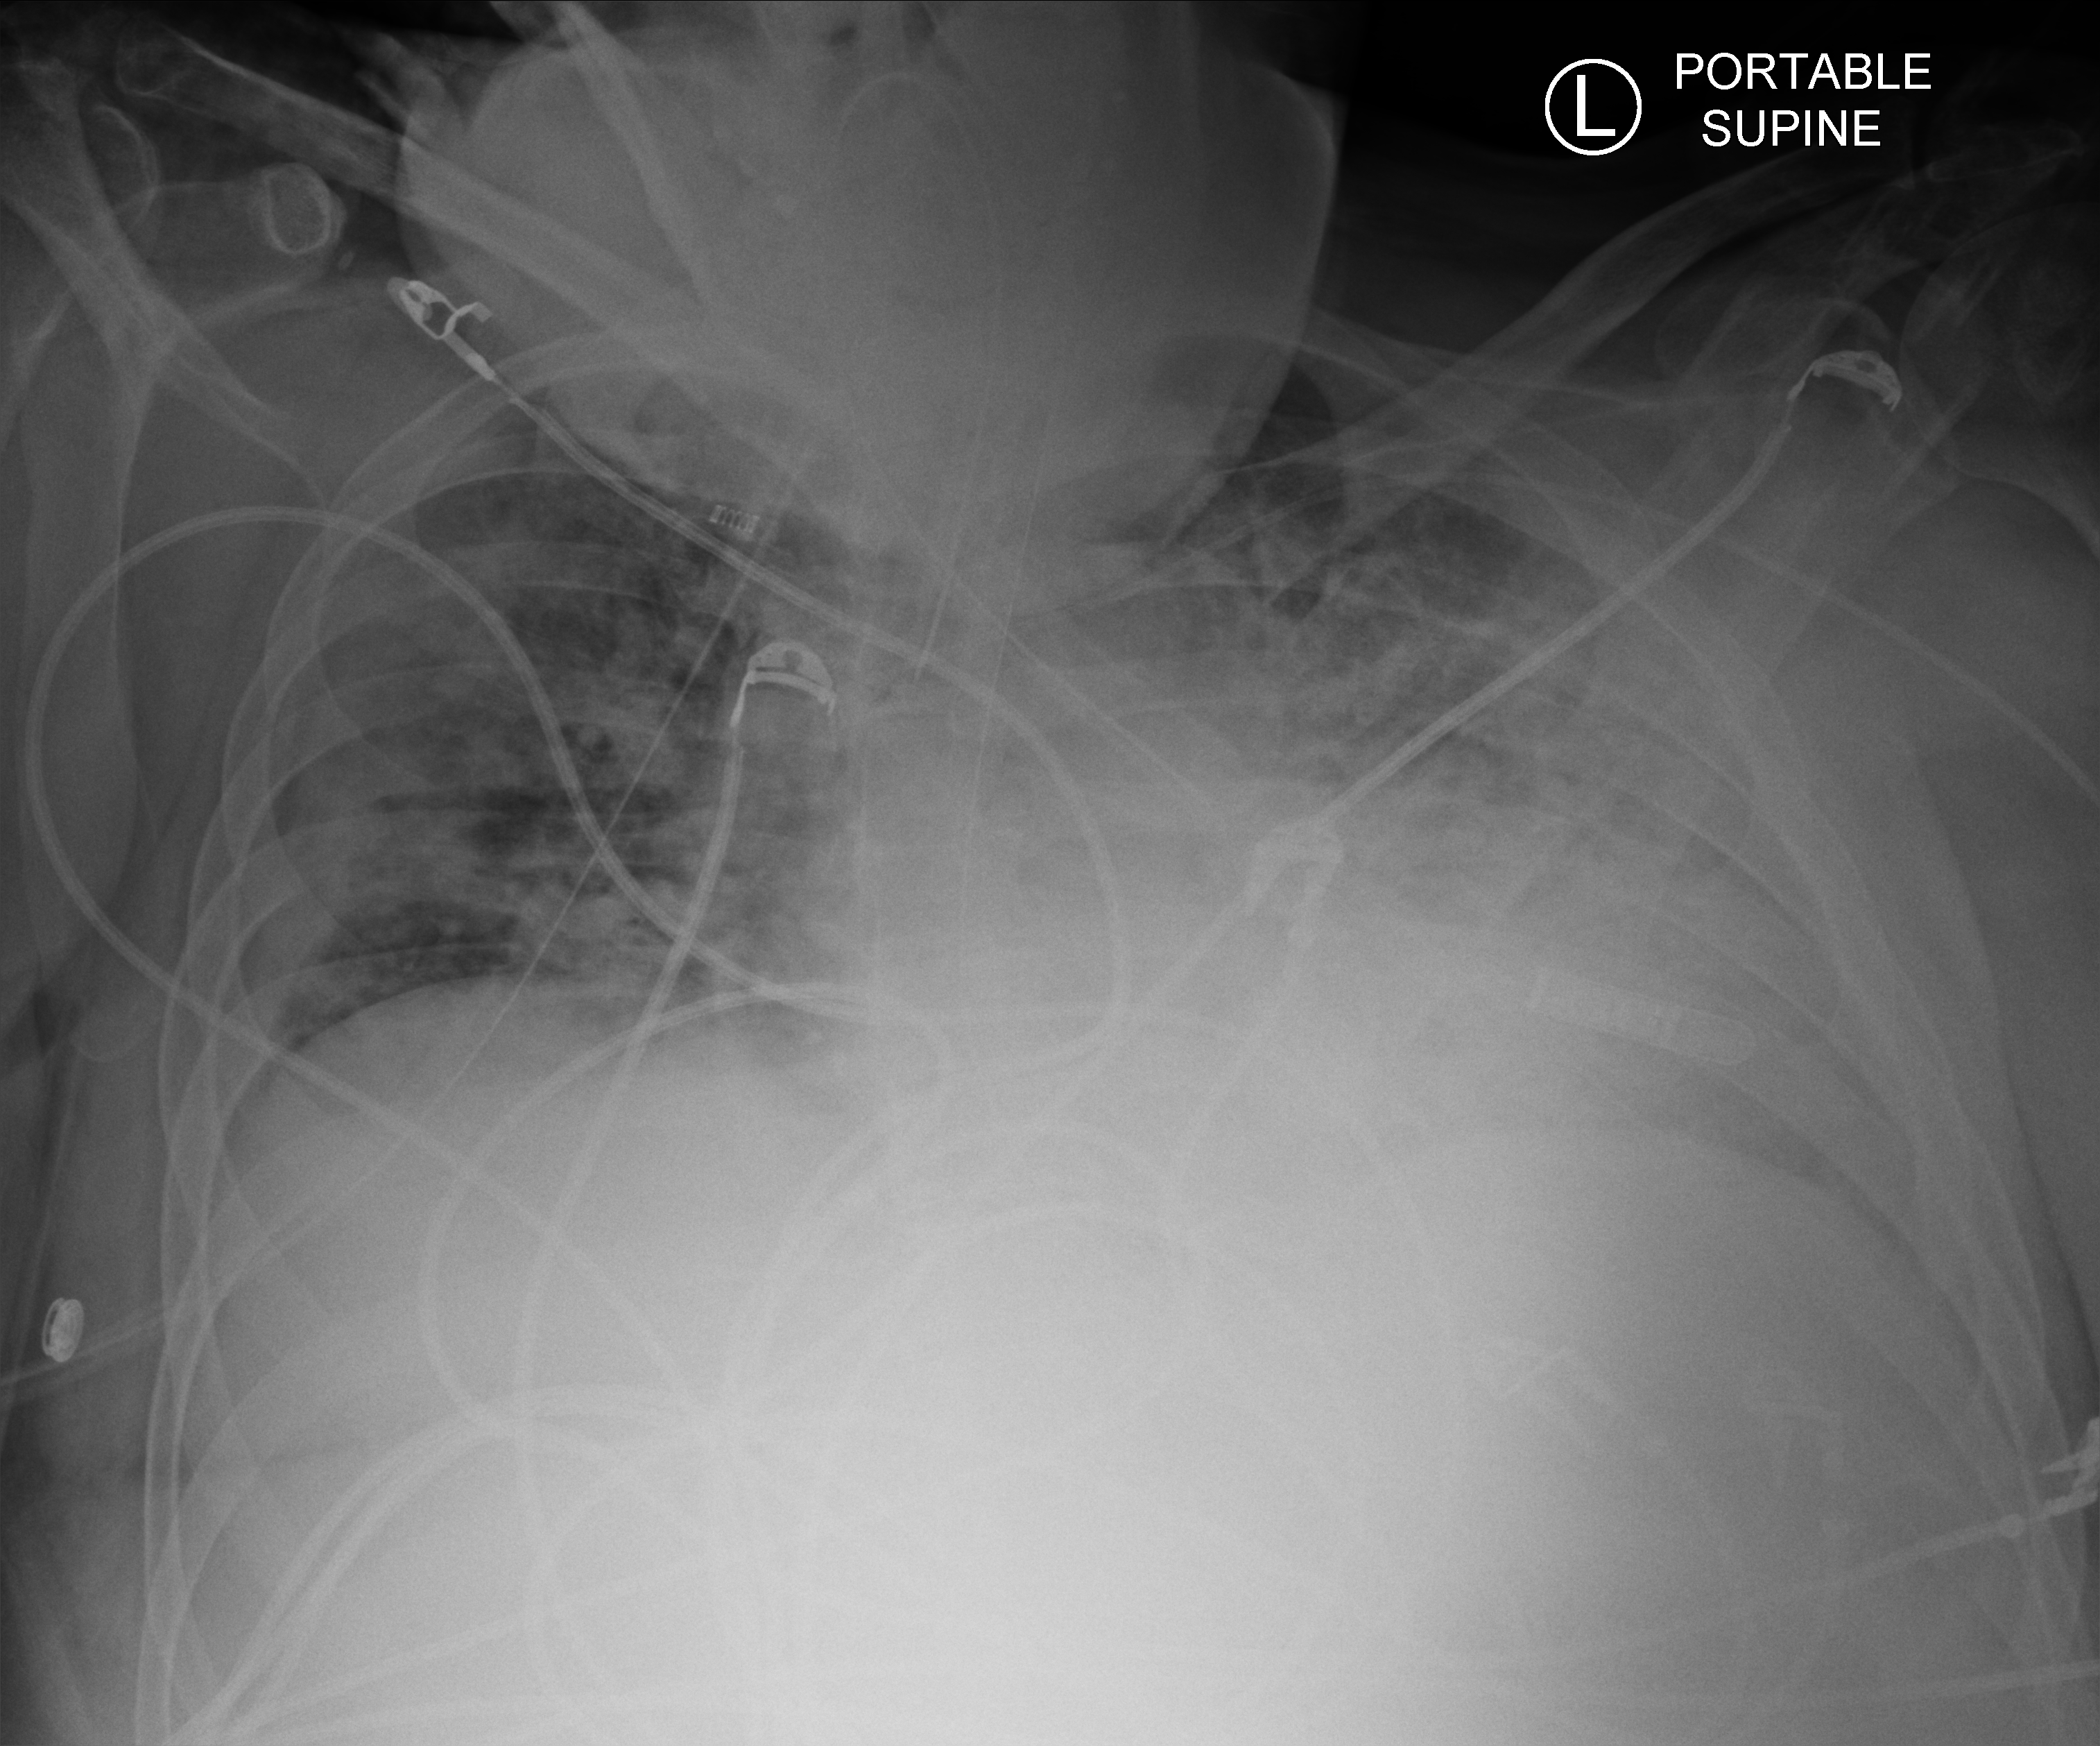
Chest X-ray (portable), anteroposterior (AP) projection. Patient hospitalised with COVID-19; male, aged 18–59 years.
From the hospital-stay record, not from the radiograph (when in the stay this image was taken is not recorded):
- admitted to intensive care during this hospital stay: yes